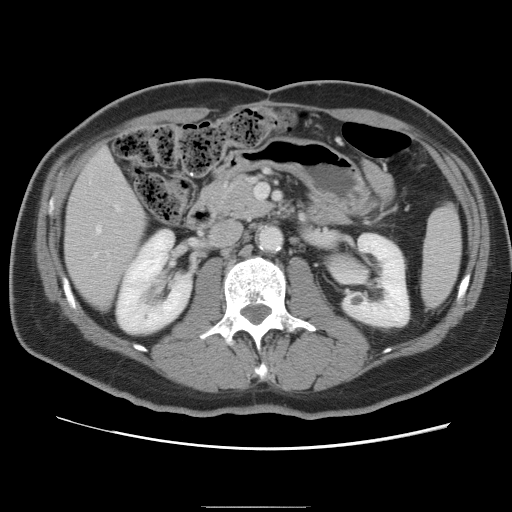
Contrast-enhanced abdominal CT, one axial slice. Position 32 of 87 along the scan axis. 120 kVp. Intravenous contrast given. Soft-tissue window (W 400 / L 40 HU). 5 mm slice thickness. 512 × 512 image matrix, field of view 363 × 363 mm. Male patient, age 63 years. Case-level facts recorded for this patient, not image findings: diagnosis: colorectal cancer liver metastases, imaged before liver resection; multiple liver metastases: no; largest metastasis: 9 cm.
Annotated regions visible in this slice (manually delineated by an expert):
- hepatic veins: bounding box [x1, y1, x2, y2] px = [95, 227, 101, 255]
- liver: [66, 151, 146, 308]
- planned liver remnant (the part of the liver to remain after resection): [66, 151, 147, 308]